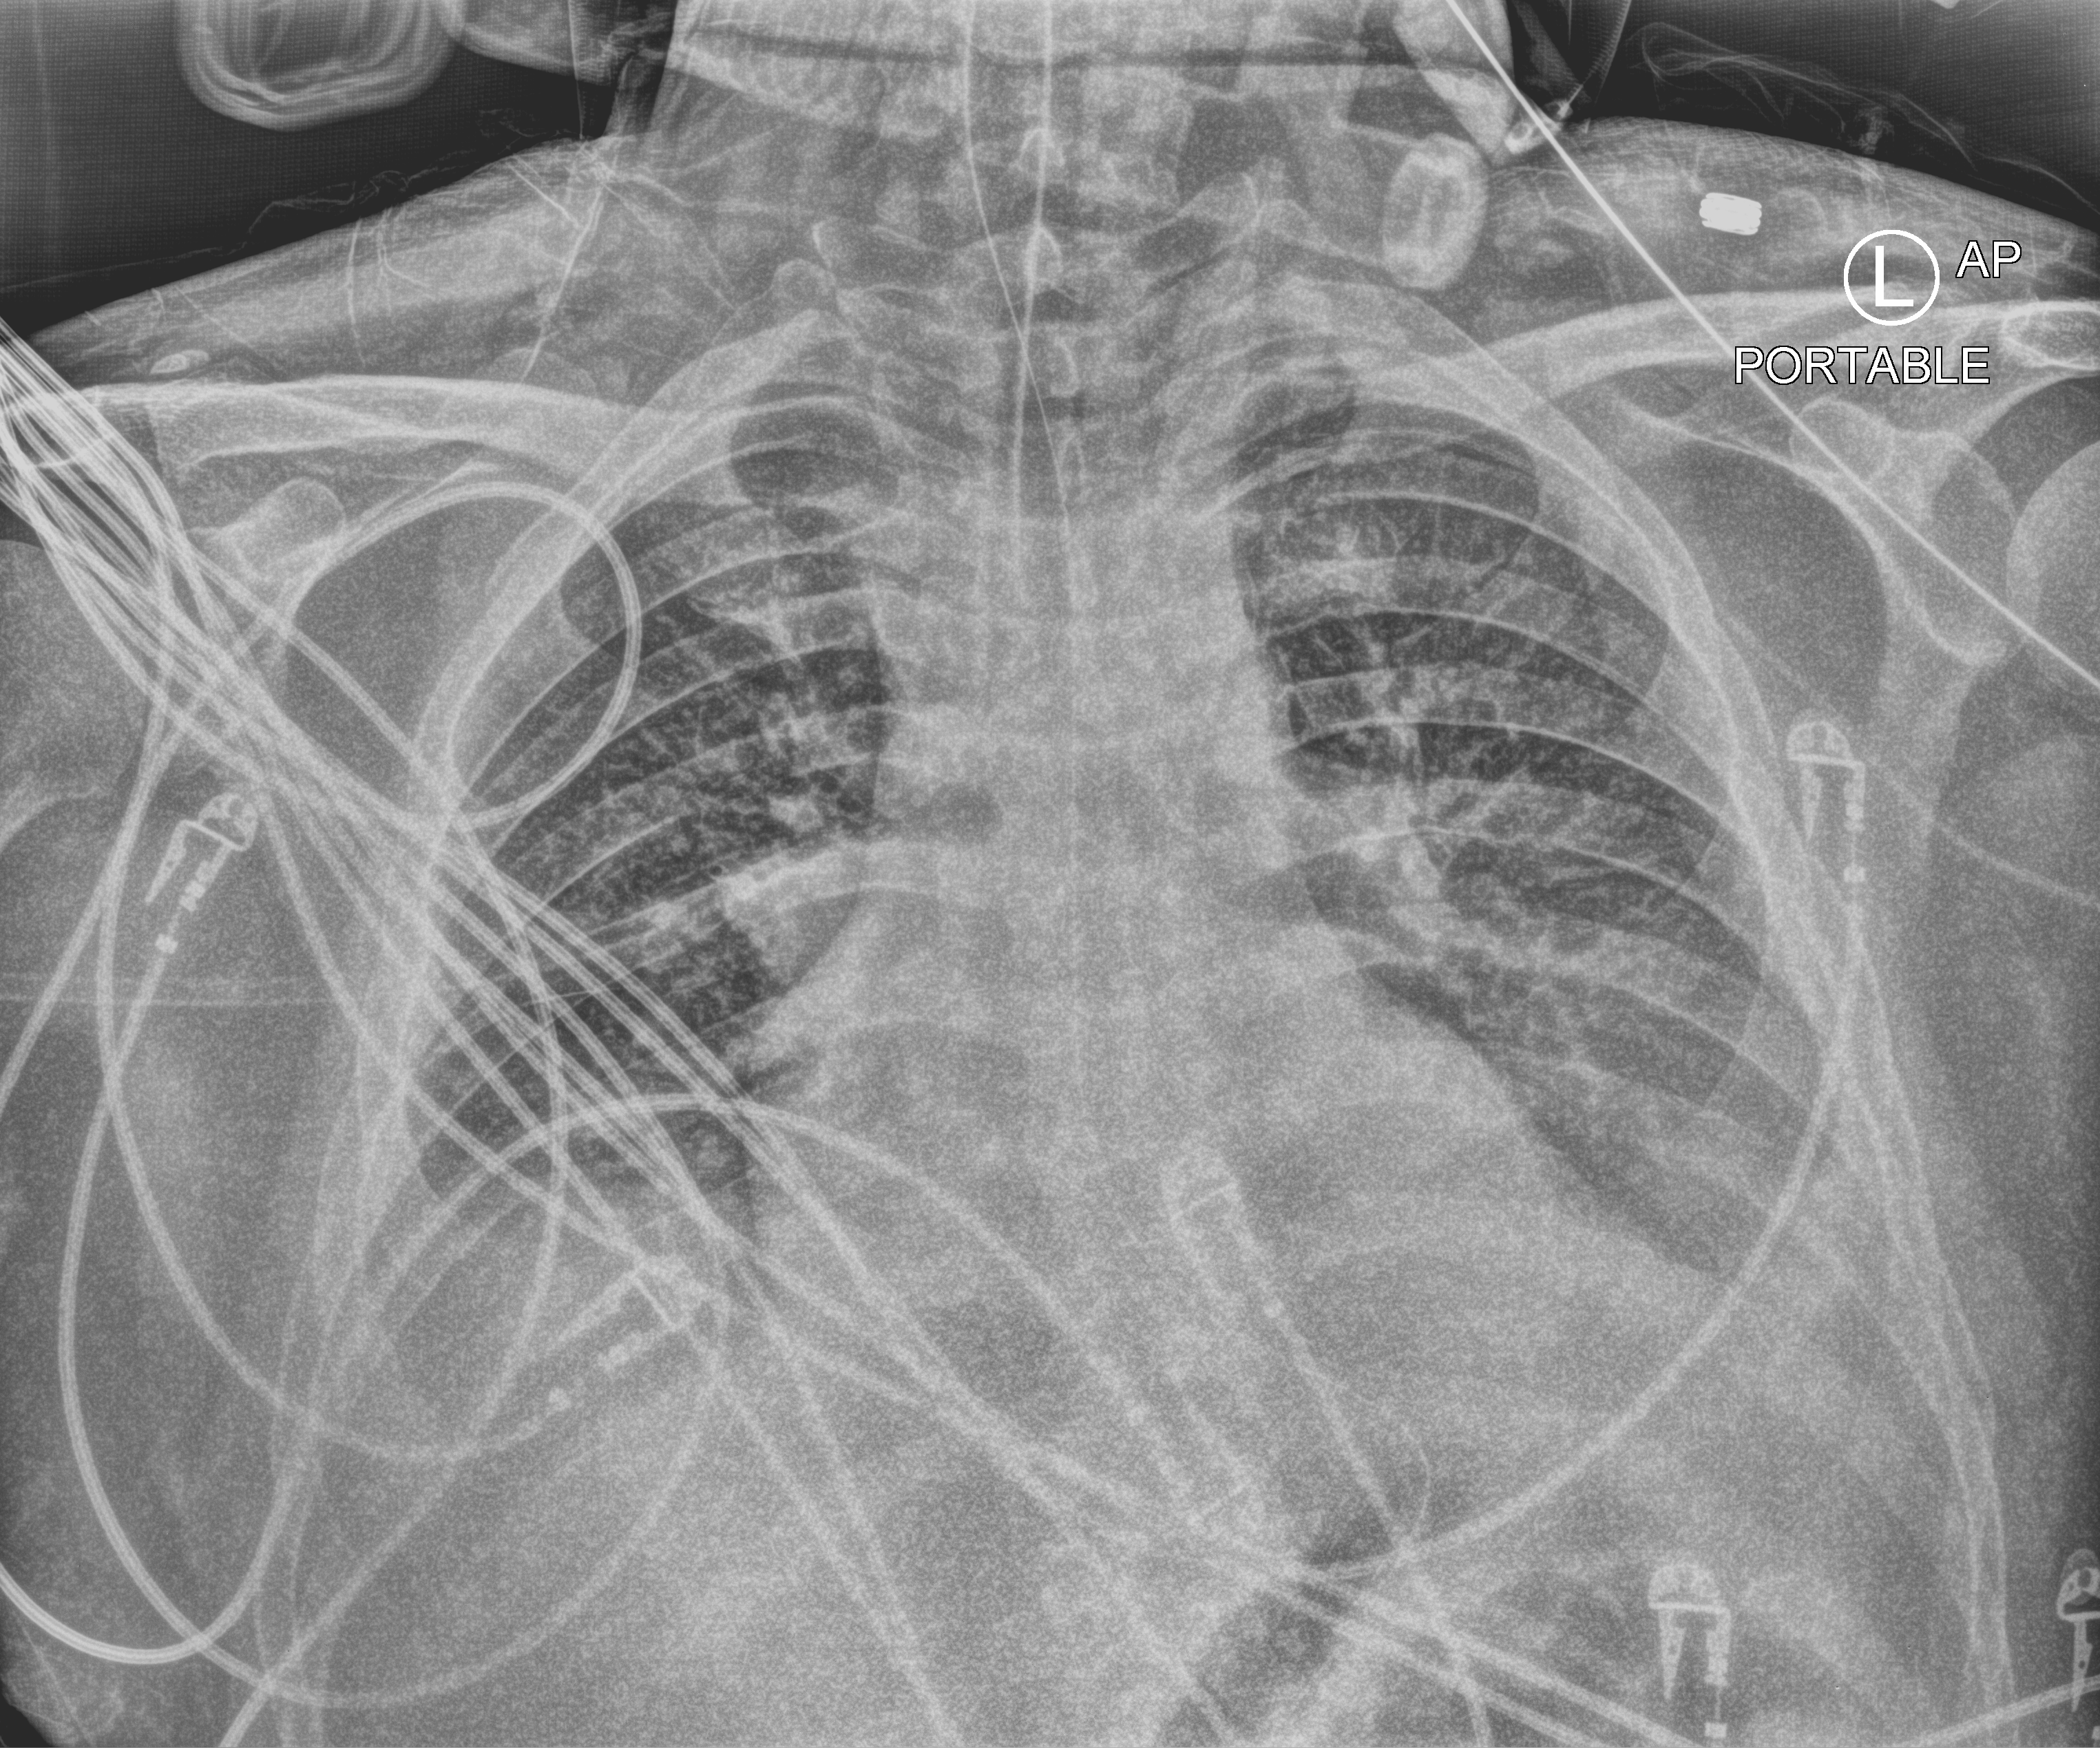
Portable chest radiograph; anteroposterior (AP) projection. Male patient hospitalised with COVID-19, age 18–59 years.
Admission-level facts for this patient (not findings on this image; timing relative to this image not recorded):
- mechanically ventilated during this hospital stay: yes
- admitted to intensive care during this hospital stay: yes